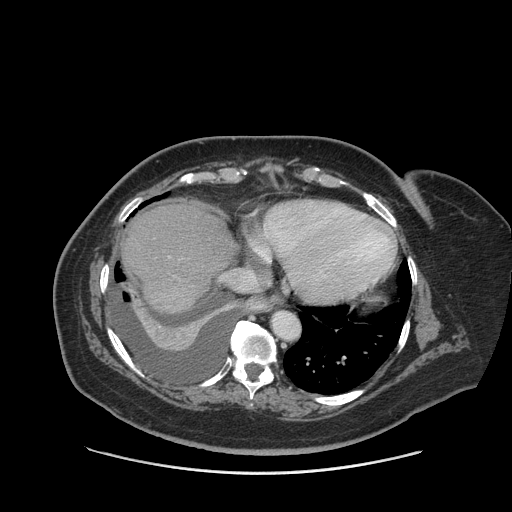
Contrast-enhanced abdominal CT (liver protocol), one axial slice. Slice 76 of 91 in the series (ordered by position). Reconstruction kernel STANDARD. Soft-tissue window (W 400 / L 40 HU). 512 × 512 image matrix, field of view 420 × 420 mm. From the clinical record (not read from this slice): diagnosis: hepatocellular carcinoma (patient treated with transarterial chemoembolisation; whether this scan precedes or follows treatment is not stated here); TNM stage (as recorded): Stage-I; Child-Pugh class: A; tumour differentiation: well differentiated; tumour nodularity: uninodular.
Outlined on this slice (semi-automatic segmentation, software-assisted and operator-edited):
- abdominal aorta: bounding box <272,312,300,340> (left, top, right, bottom; pixels)
- liver parenchyma outside the tumour (the mass and vessels are separate outlines, so this box may not span the whole liver): <122,200,236,314>